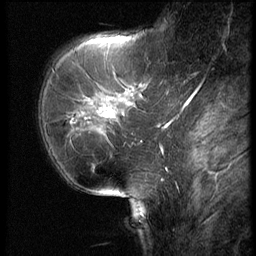
Breast MRI (dynamic contrast-enhanced), one sagittal slice. Position 20 of 62 along the scan axis. 3 images stored at this slice position (order not interpretable as contrast timing). 1.5 T. TE 4.2 ms, TR 9 ms. 2.5 mm slice thickness. 256 × 256 image matrix, field of view 180 × 180 mm. Patient: female, 62 years. From the clinical record (not read from this slice): setting: breast cancer imaged before/during neoadjuvant chemotherapy; receptor status: HR-positive, HER2-negative.
Structures marked on this image (semi-automatically segmented with operator editing):
- analysis volume of interest (the breast-tissue region the enhancement analysis was run in; not a lesion): bounding box (x1, y1, x2, y2) in pixels: (56, 62, 154, 155)
- tumour enhancement mask (voxels above the 140 % enhancement threshold inside the analysis volume of interest): (99, 110, 114, 118)